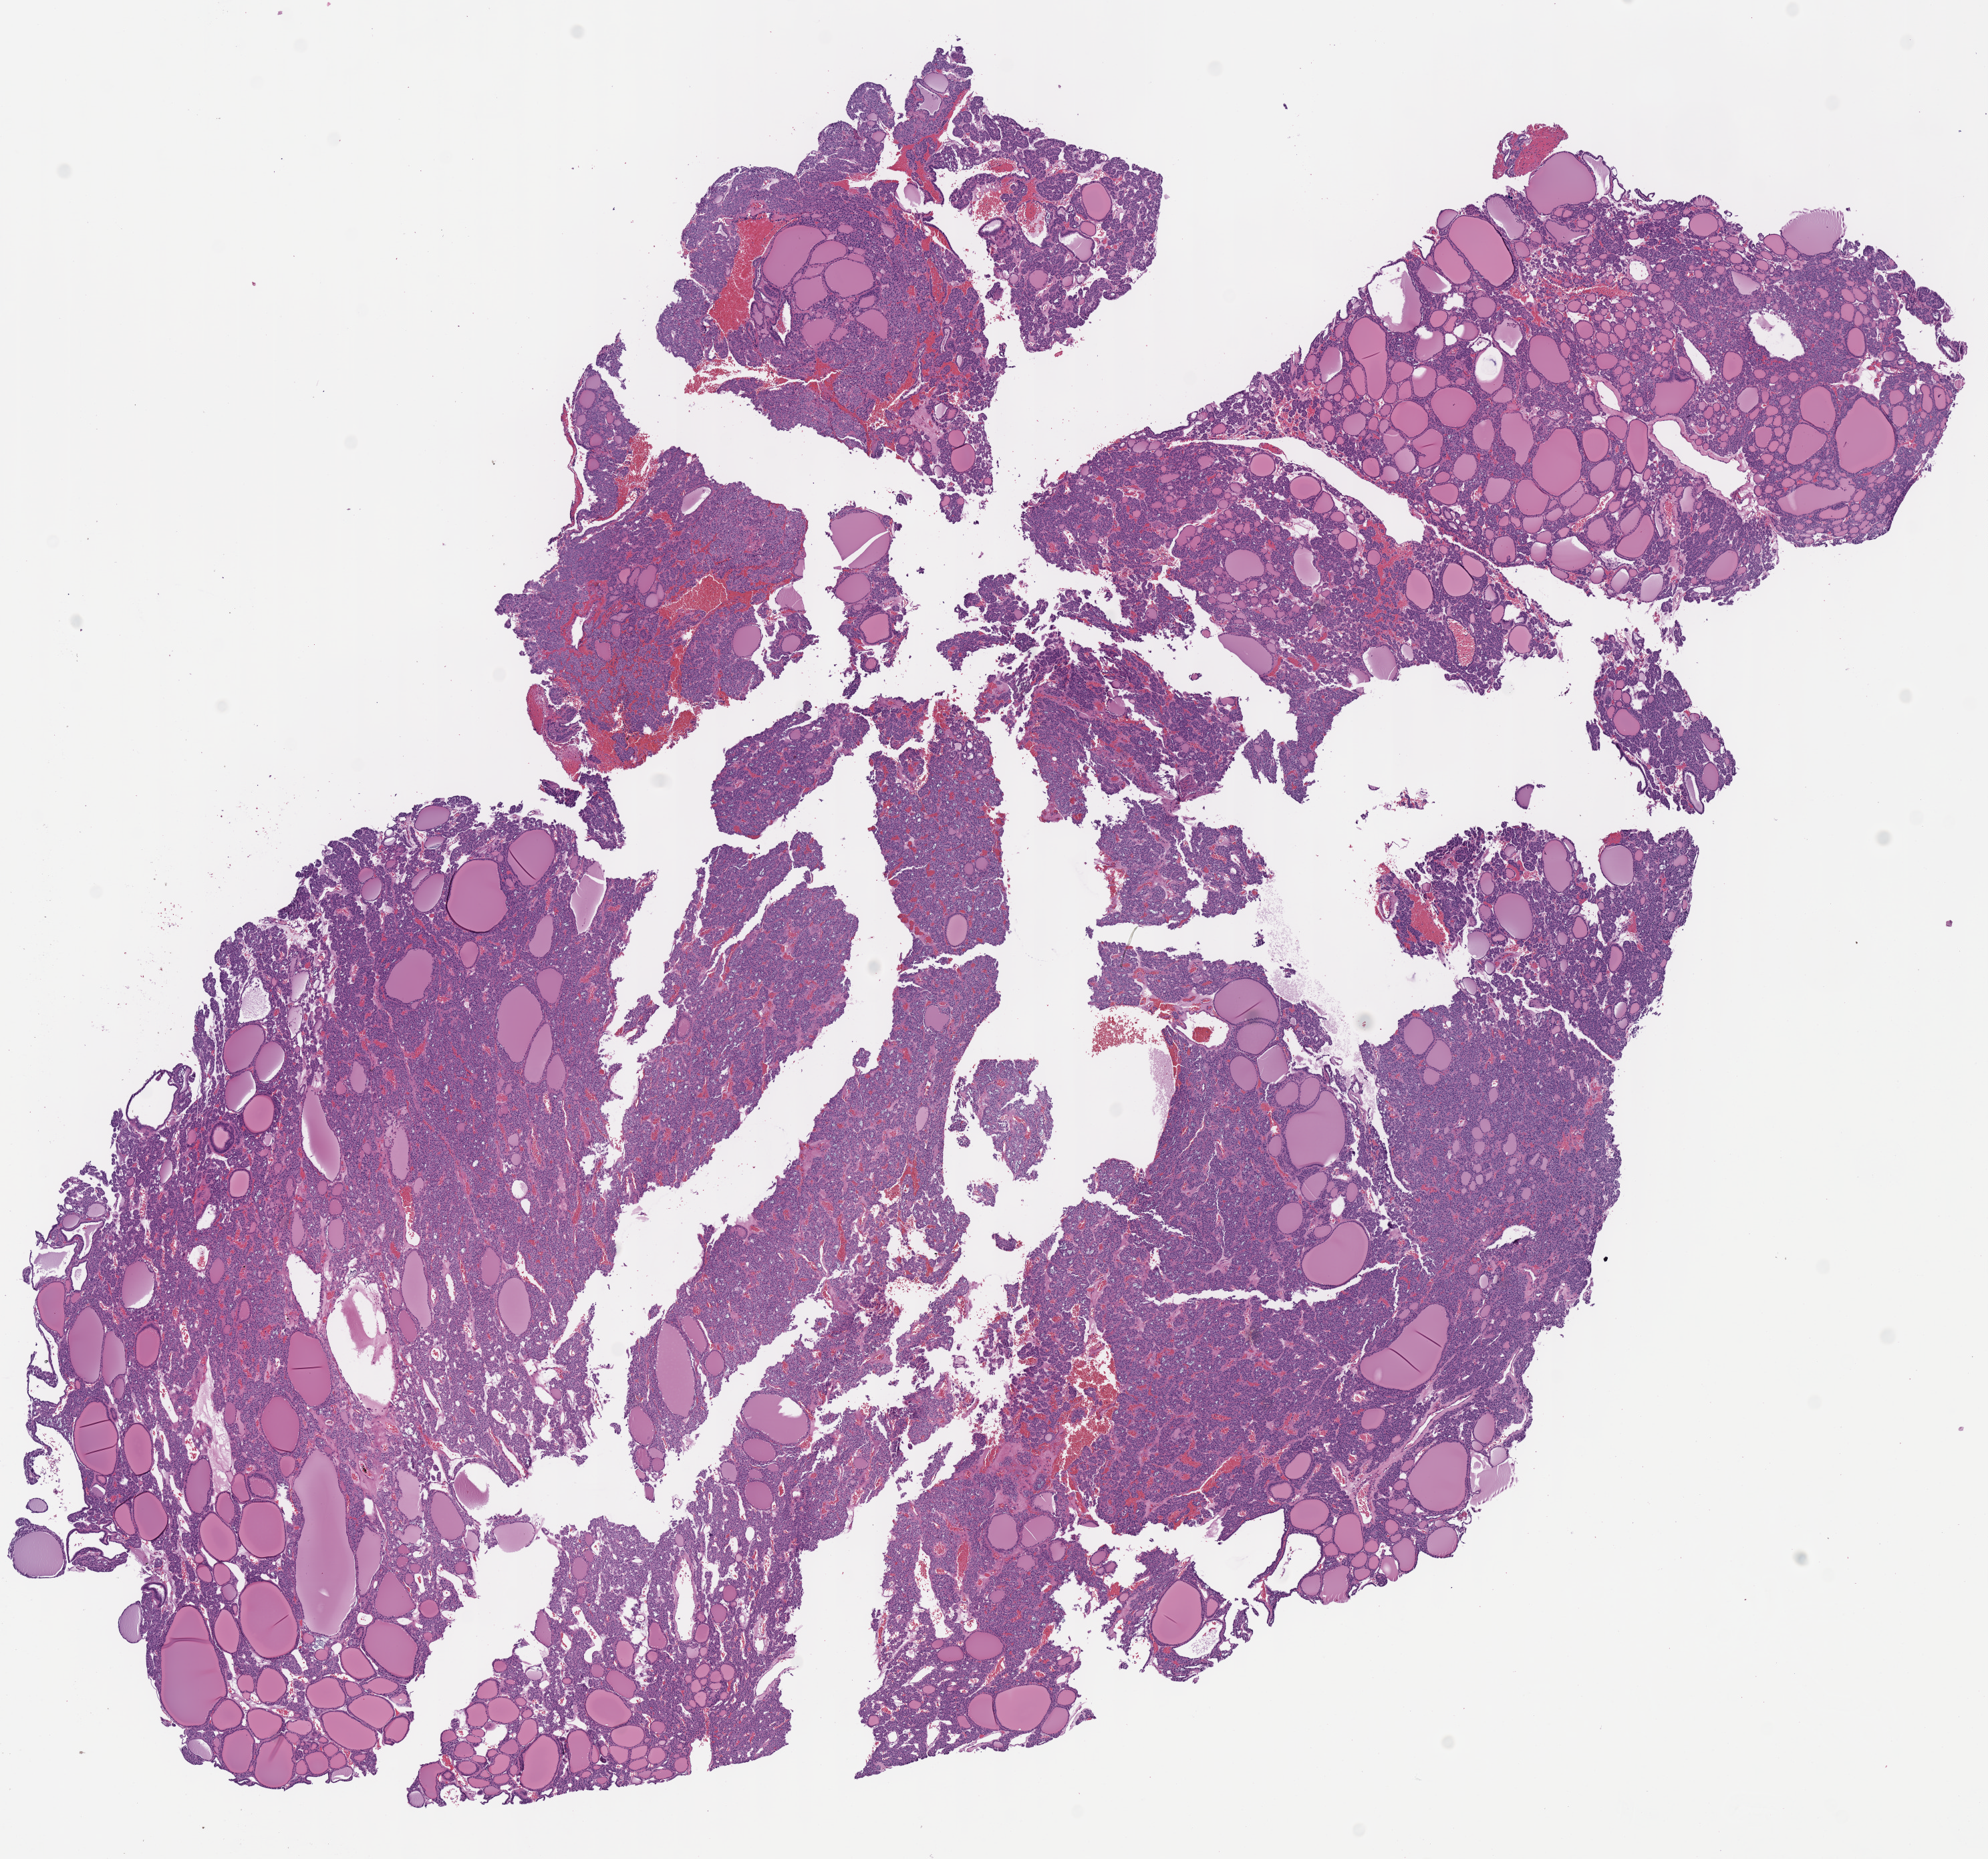
Hematoxylin and eosin (H&E) stained whole-slide image, shown as a low-resolution overview of the whole scanned area (about 11.7 x 11.0 mm, from a 40x scan). Formalin-fixed paraffin-embedded (FFPE) diagnostic section. Primary tumour sample from the thyroid. Female, age 61 years at initial diagnosis.
Lymph nodes positive (case pathology): 0 of 3 examined. Pathologic diagnosis: Papillary adenocarcinoma, NOS (thyroid gland).